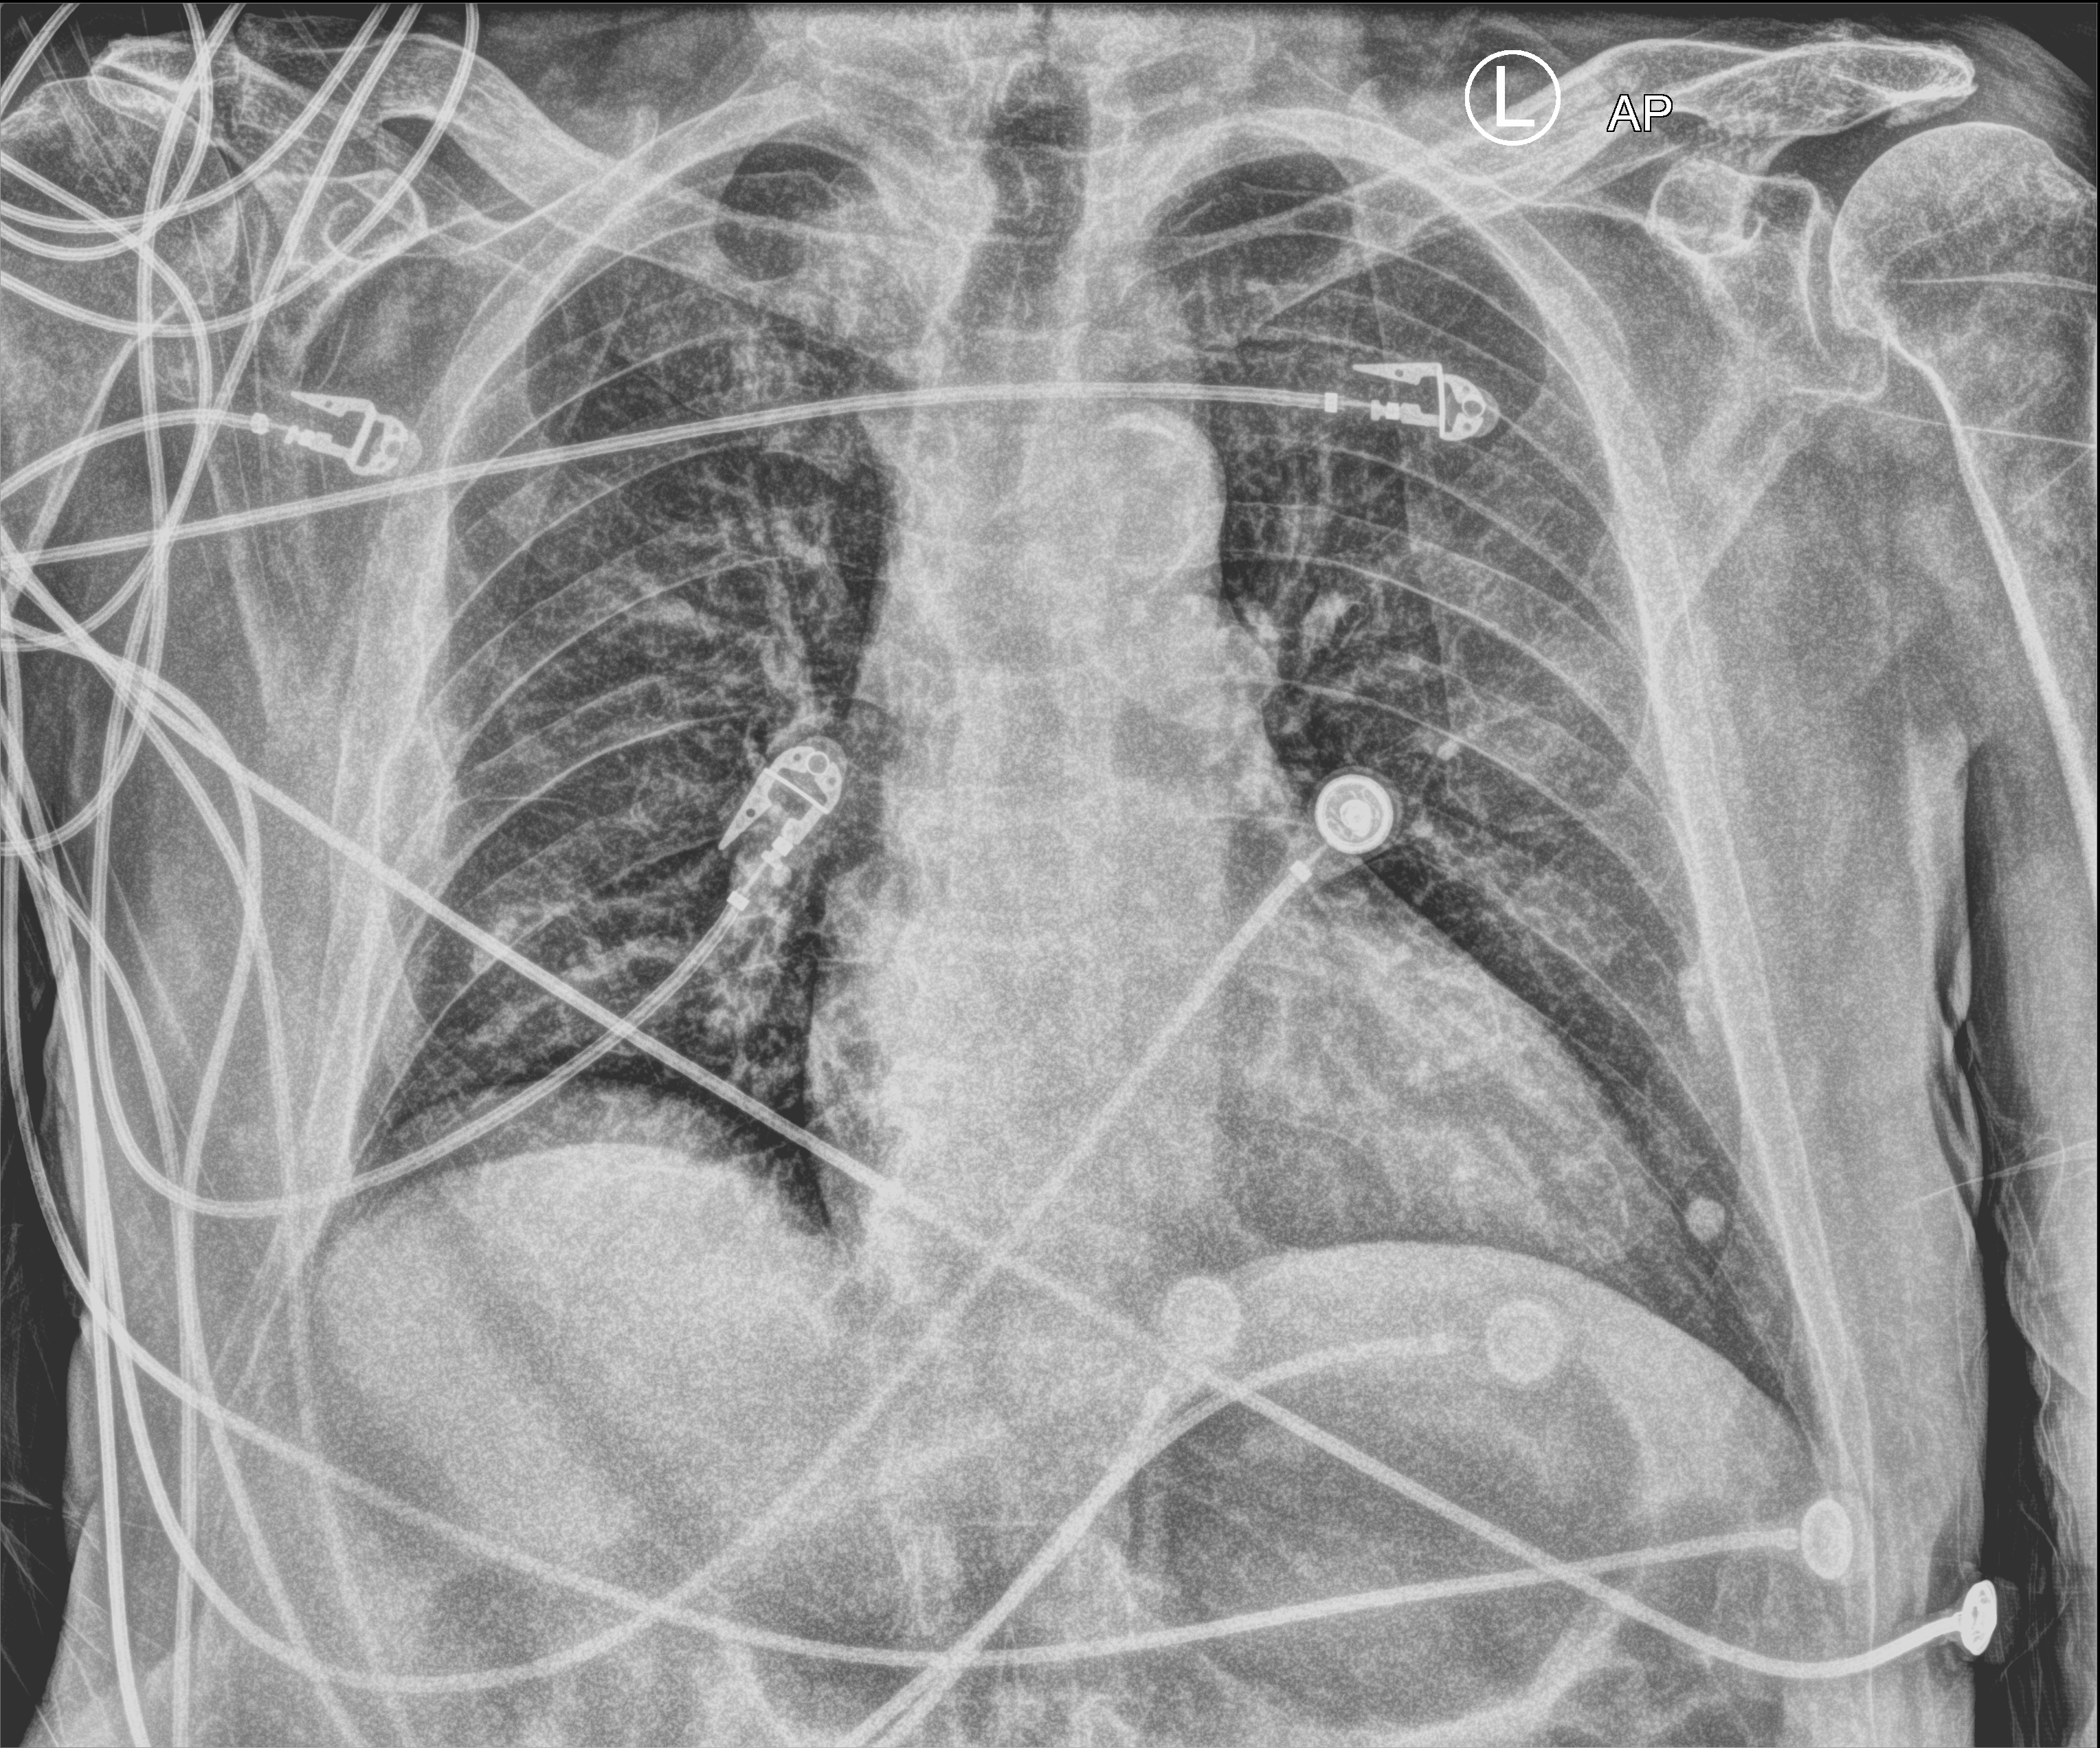
Portable chest radiograph, anteroposterior (AP) projection. Patient hospitalised with COVID-19; male, aged 75–90 years.
Admission-level facts for this patient (not findings on this image; timing relative to this image not recorded): mechanically ventilated during this hospital stay: no; diabetes (admission record): yes.